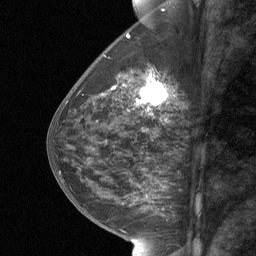
Breast MRI (dynamic contrast-enhanced), one sagittal slice; position 27 of 64 along the scan axis; dynamic contrast-enhanced study with each time point stored as its own series, time point 2 of 3 at this slice position (early post-contrast, ordered by acquisition time); 1.5 T; TE 4.8 ms, TR 27 ms; 2 mm slice thickness; 256 × 256 image matrix, field of view 180 × 180 mm. Female patient, age 59 years. From the clinical record (not read from this slice): setting: breast cancer imaged before/during neoadjuvant chemotherapy; receptor status: triple-negative.
Outlined on this slice (semi-automatic segmentation, software-assisted and operator-edited):
- analysis volume of interest (the breast-tissue region the enhancement analysis was run in; not a lesion): box from (x=127, y=66) to (x=171, y=122) px
- tumour enhancement mask (voxels above the 90 % enhancement threshold inside the analysis volume of interest): (x=136, y=79)–(x=168, y=105)